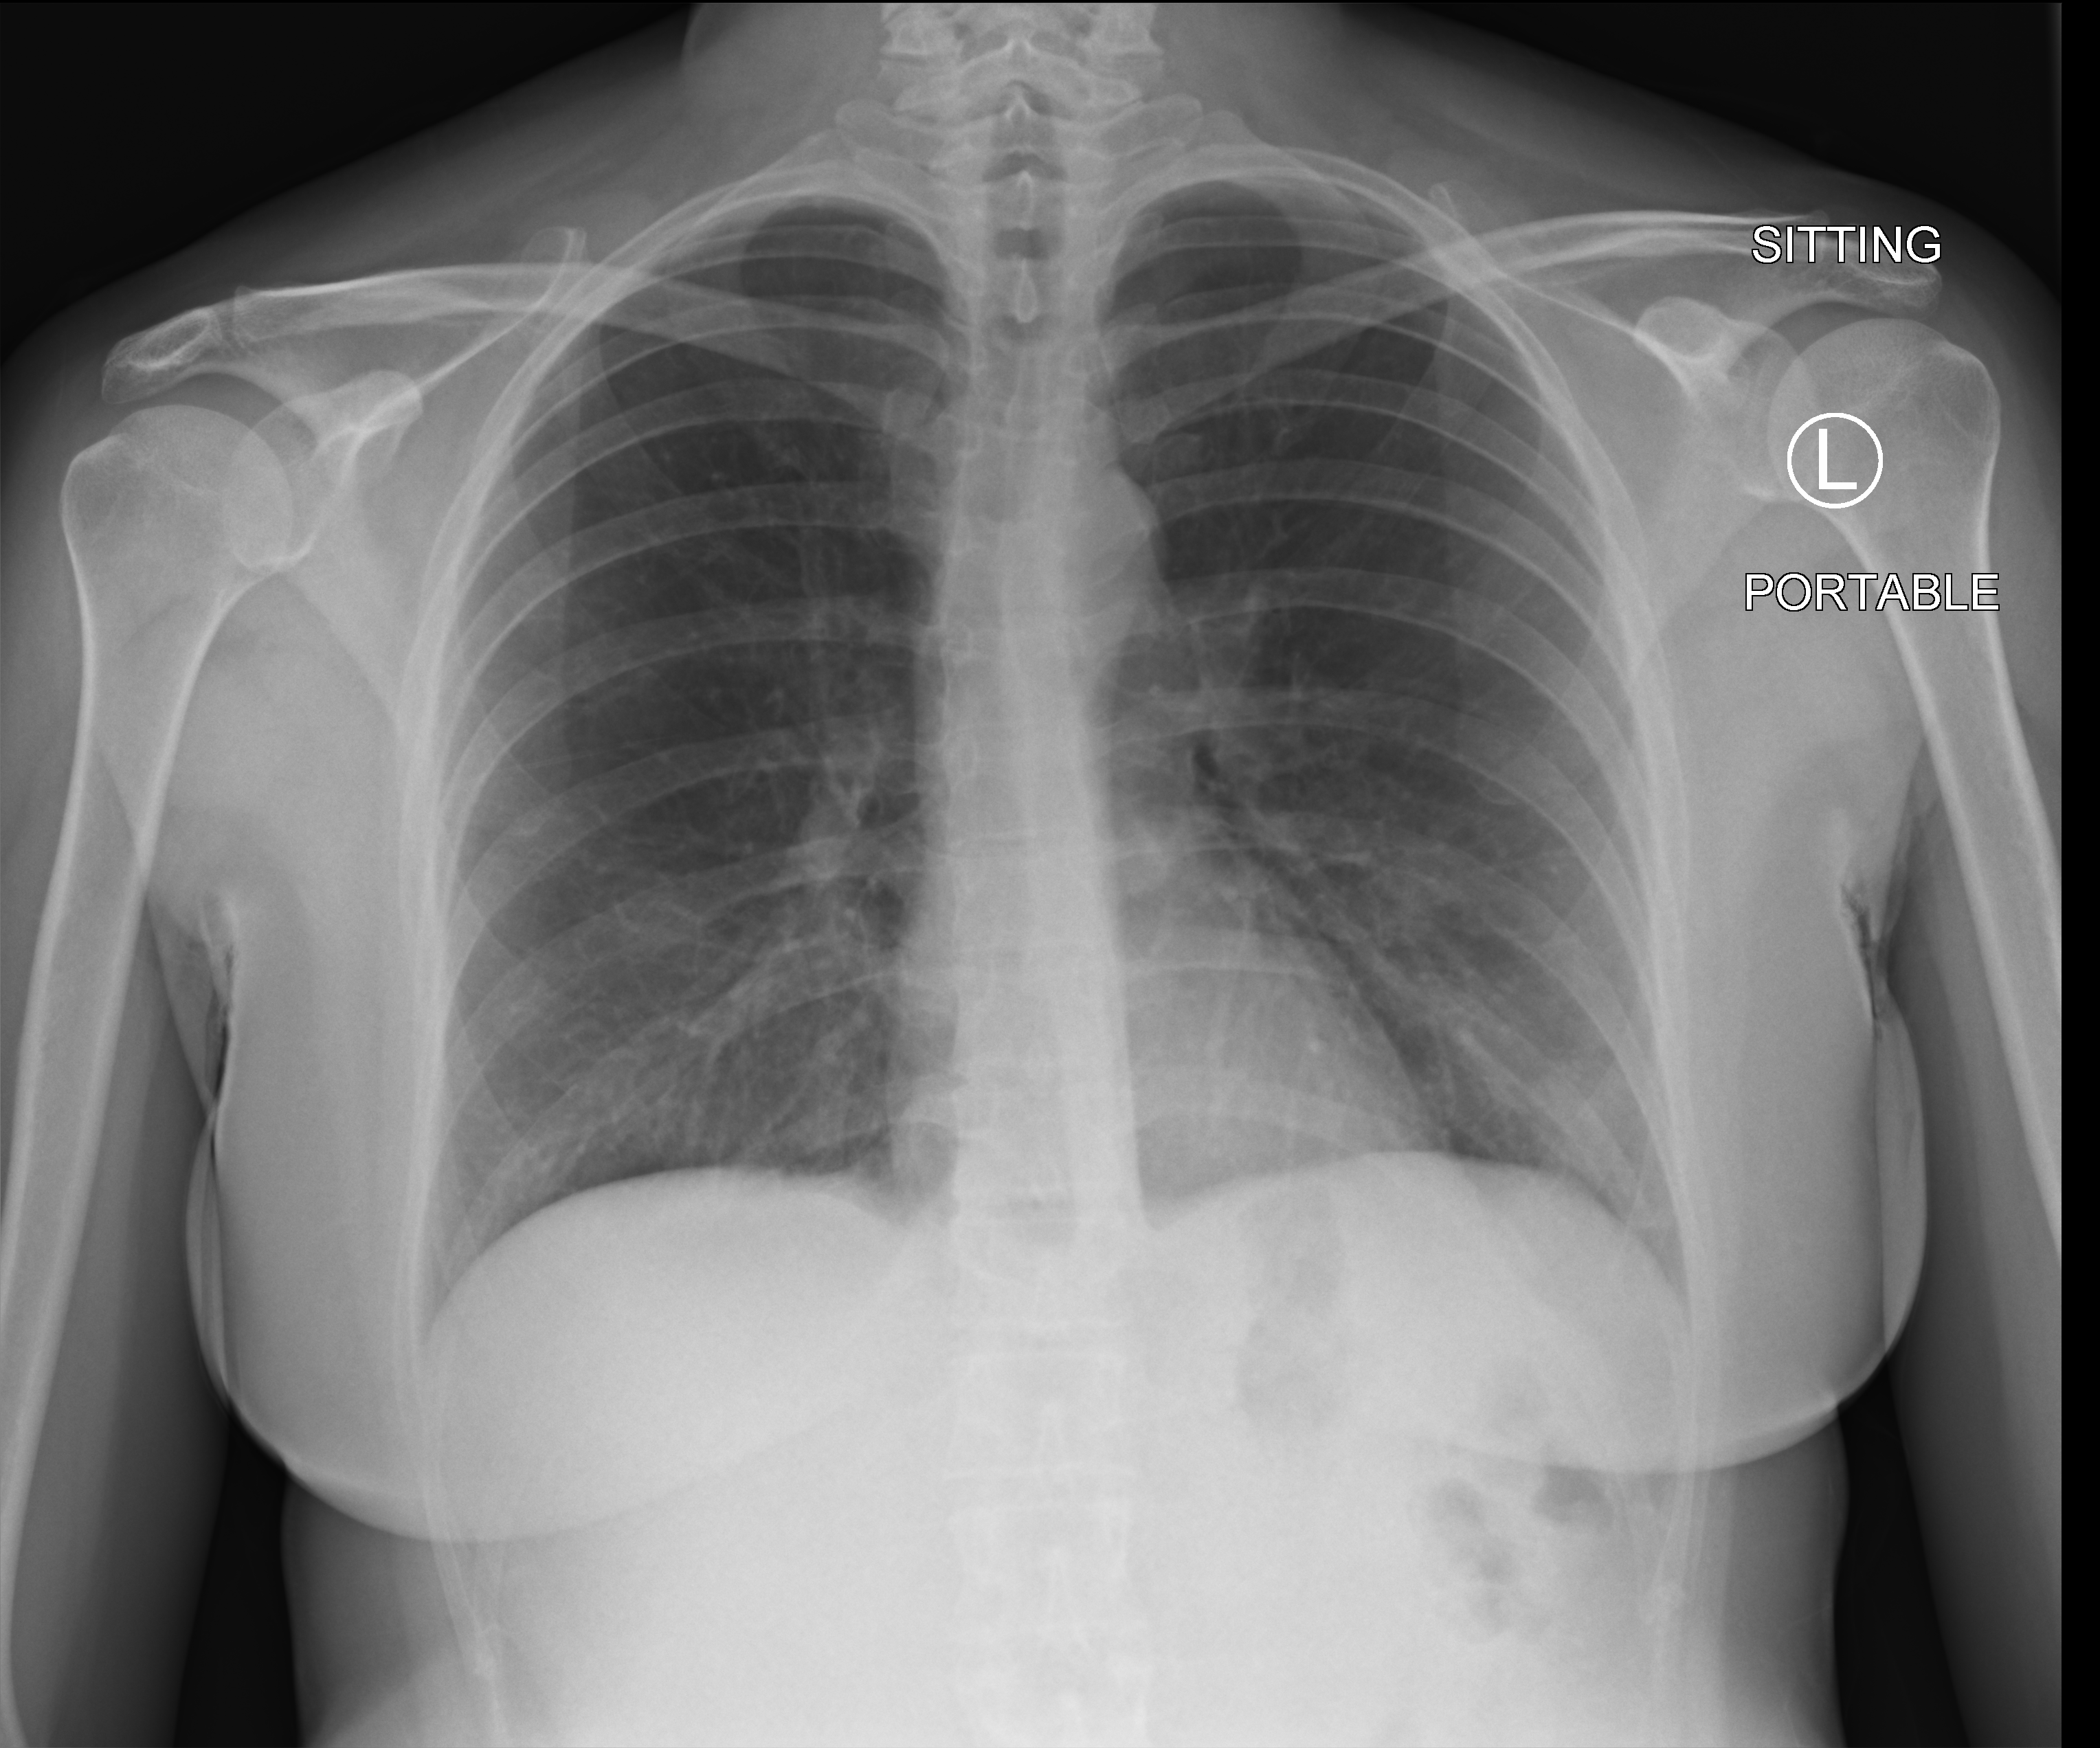
Bedside chest radiograph (computed radiography); anteroposterior (AP) projection. Female patient hospitalised with COVID-19, age 18–59 years.
From the hospital-stay record, not from the radiograph (when in the stay this image was taken is not recorded): admitted to intensive care during this hospital stay: no; mechanically ventilated during this hospital stay: no.